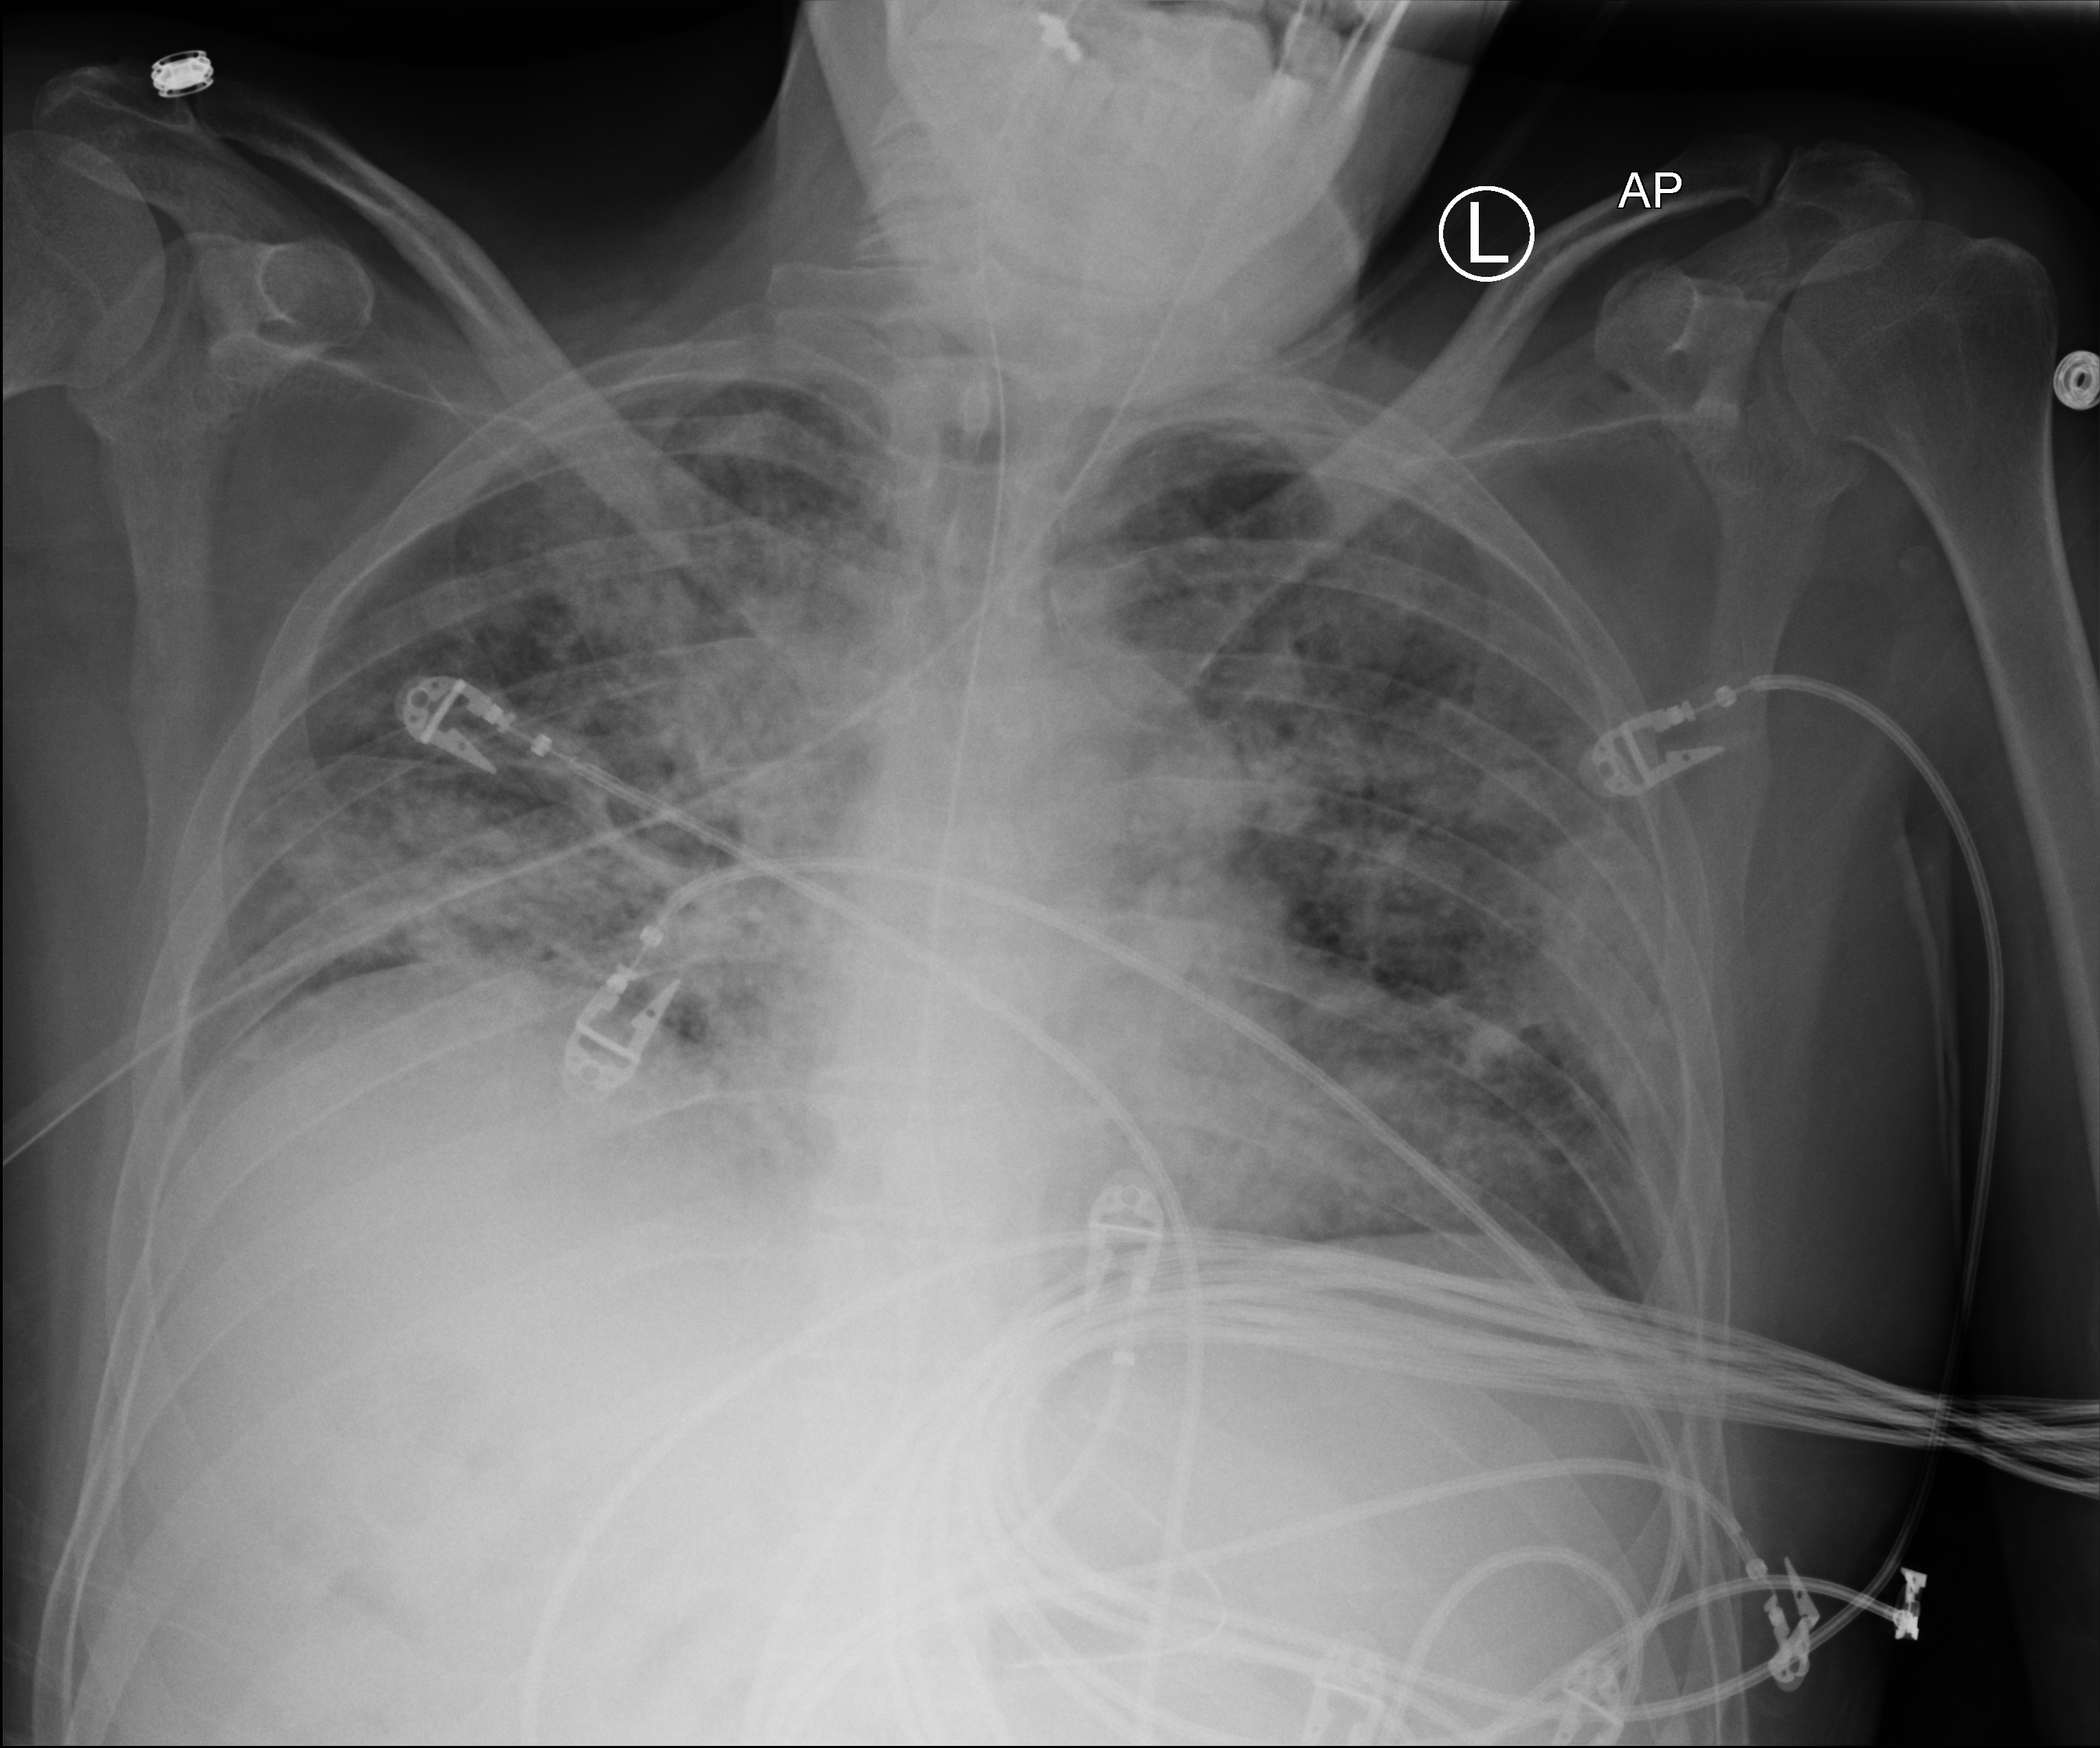
Chest X-ray (portable); anteroposterior (AP) projection. Male patient hospitalised with COVID-19, age 18–59 years.
Hospital-stay facts (about this admission, not read from this image; timing relative to this image not recorded):
- length of hospital stay: 48 days